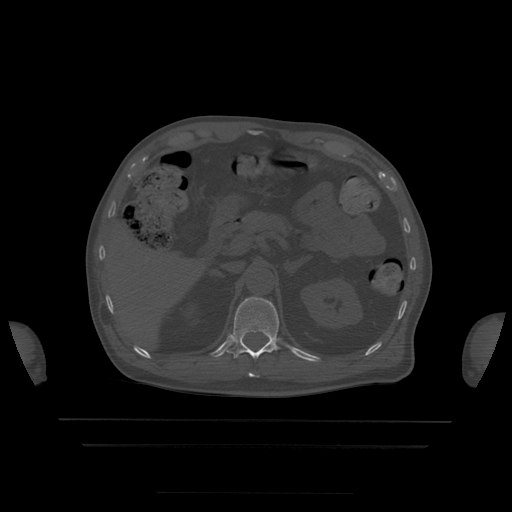
CT including the spine, one axial slice. Slice 196 of 522 in the series (ordered by position). Bone window (W 1800 / L 400 HU). 512 × 512 image matrix, field of view 436 × 436 mm. Patient age 68 years. From the clinical record (not read from this slice): primary cancer: urothelial.
Outlined on this slice (semi-automatically segmented with operator editing):
- T11 vertebra: bounding box [x1, y1, x2, y2] px = [248, 373, 259, 378]
- T12 vertebra: [226, 297, 280, 359]